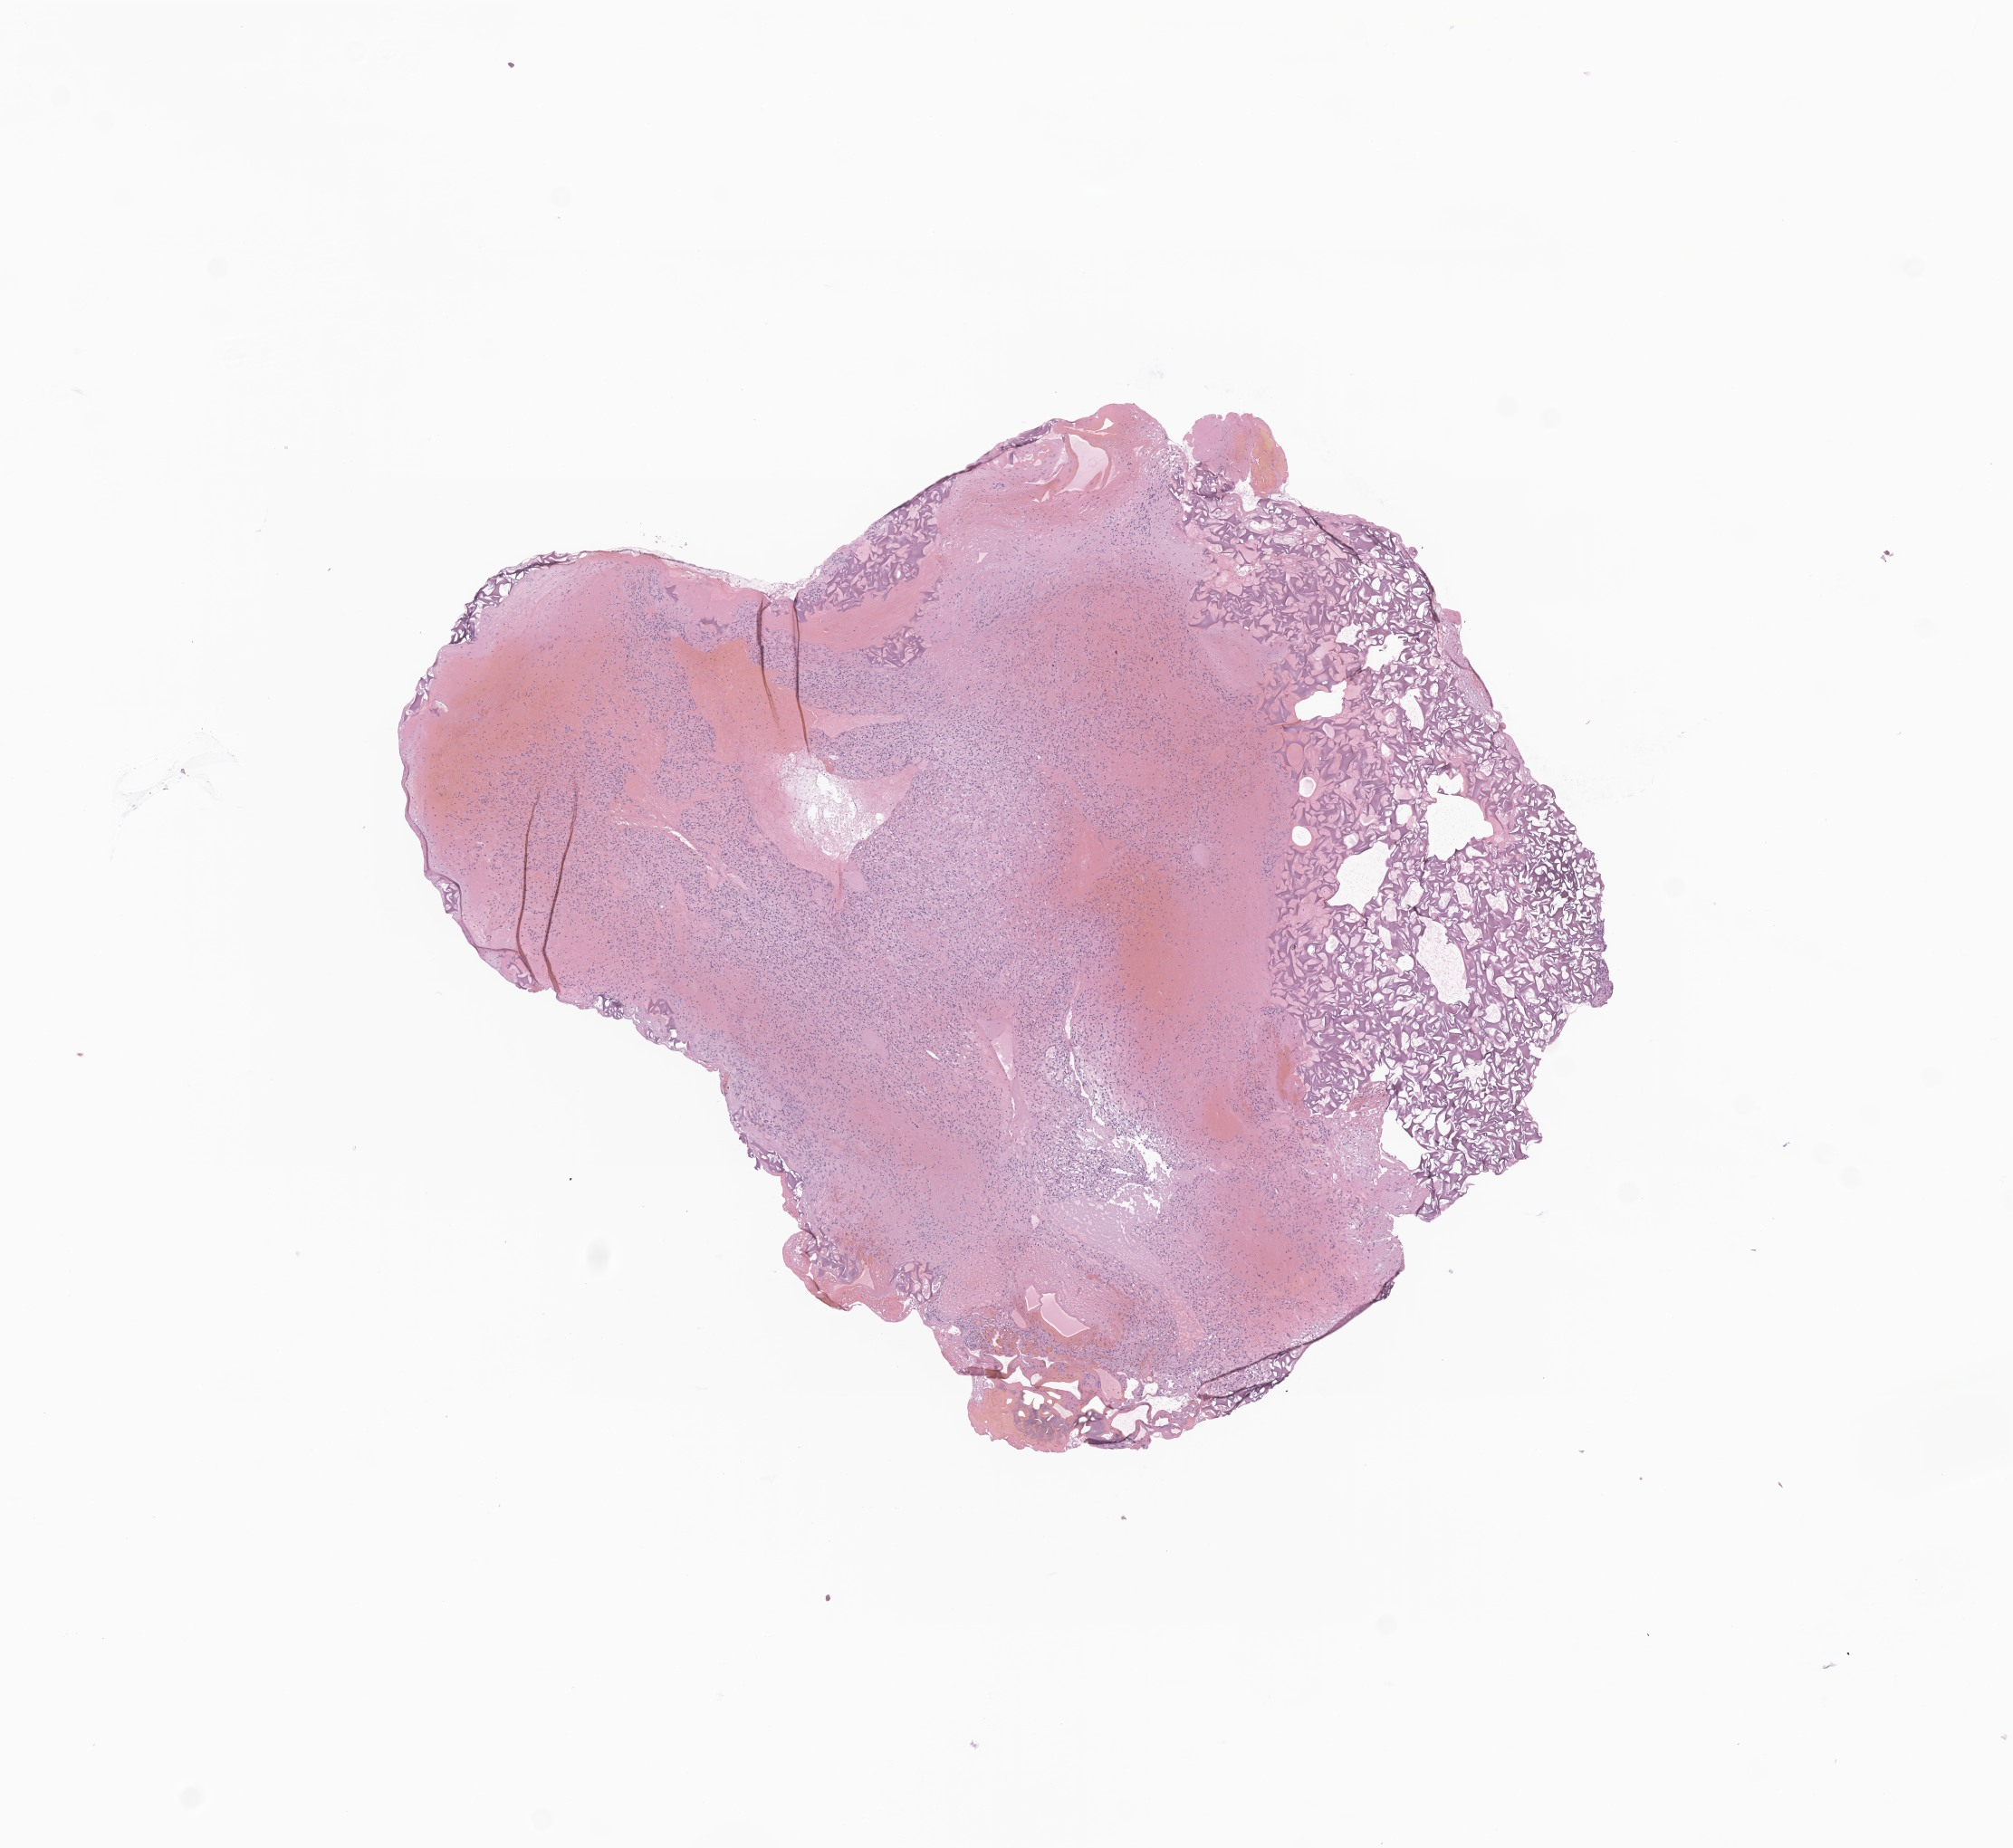
Digitized haematoxylin and eosin-stained section of tumor tissue from the brain — whole scanned area (about 9.4 x 8.6 mm) shown as a low-resolution overview, FFPE section. Male patient, age 170 months (14 years 2 months).
Recorded diagnosis: Hemangioblastoma.